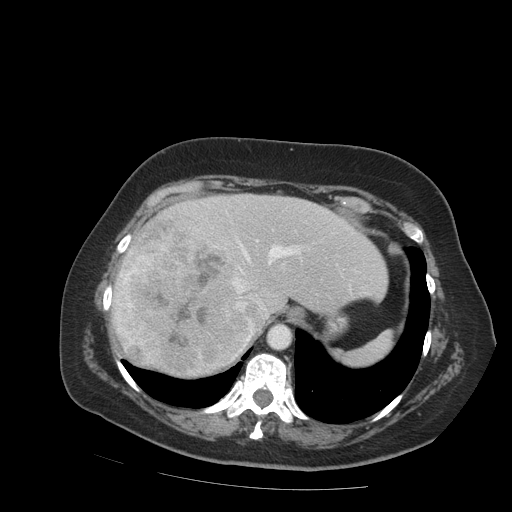
Contrast-enhanced abdominal CT (liver protocol), one axial slice. 140 kVp. Soft-tissue window (W 400 / L 40 HU). 2.5 mm slice thickness. 512 × 512 image matrix, field of view 400 × 400 mm. Case-level facts recorded for this patient, not image findings: diagnosis: hepatocellular carcinoma (patient treated with transarterial chemoembolisation; whether this scan precedes or follows treatment is not stated here); TNM stage (as recorded): Stage-IVB; Child-Pugh class: A; tumour differentiation: moderately differentiated.
Annotated regions visible in this slice (semi-automatic segmentation, software-assisted and operator-edited):
- abdominal aorta: bounding box (x1, y1, x2, y2) in pixels: (267, 324, 291, 349)
- liver parenchyma outside the tumour (the mass and vessels are separate outlines, so this box may not span the whole liver): (112, 194, 388, 366)
- mass: (110, 225, 264, 379)
- liver vessels: (214, 240, 300, 308)